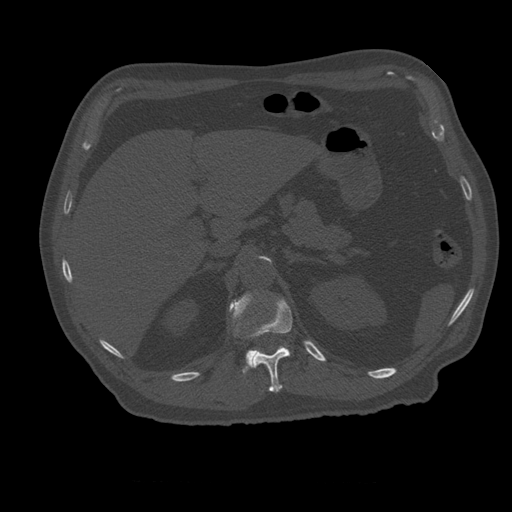
CT including the spine, one axial slice; slice 255 of 399 in the series (ordered by position); reconstruction kernel STANDARD; 120 kVp; bone window (W 1800 / L 400 HU); 512 × 512 image matrix. Patient age 73 years. Case-level facts recorded for this patient, not image findings: primary cancer: prostate.
Annotated regions visible in this slice (semi-automatically segmented with operator editing):
- L1 vertebra: bounding box (x1, y1, x2, y2) in pixels: (230, 294, 291, 374)
- T12 vertebra: (251, 299, 293, 393)